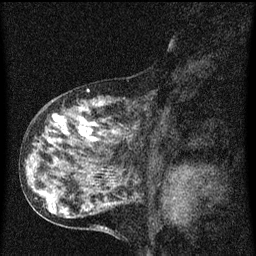
Breast MRI (dynamic contrast-enhanced), one sagittal slice. Slice 28 of 60 in the series (ordered by position). Dynamic contrast-enhanced series, image 2 of 3 at this slice position (ordered by acquisition). 1.5 T. TE 4.2 ms, TR 8 ms. 256 × 256 image matrix, field of view 180 × 180 mm. Female patient, age 55 years.
Structures marked on this image (semi-automatically segmented with operator editing):
- analysis volume of interest (the breast-tissue region the enhancement analysis was run in; not a lesion): bounding box (x1, y1, x2, y2) in pixels: (38, 92, 175, 159)
- tumour enhancement mask (voxels above the 70 % enhancement threshold inside the analysis volume of interest): (48, 114, 117, 143)